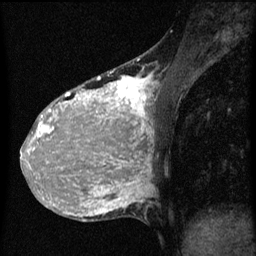
Breast MRI (dynamic contrast-enhanced), one sagittal slice; dynamic contrast-enhanced series, image 2 of 3 at this slice position (ordered by acquisition); 1.5 T; TE 4.2 ms, TR 8 ms; 2 mm slice thickness; 256 × 256 image matrix. Patient: female, 36 years.
Annotated regions visible in this slice (semi-automatic segmentation, software-assisted and operator-edited):
- analysis volume of interest (the breast-tissue region the enhancement analysis was run in; not a lesion): bounding box (x1, y1, x2, y2) in pixels: (32, 68, 161, 161)
- tumour enhancement mask (voxels above the 70 % enhancement threshold inside the analysis volume of interest): (32, 72, 153, 161)